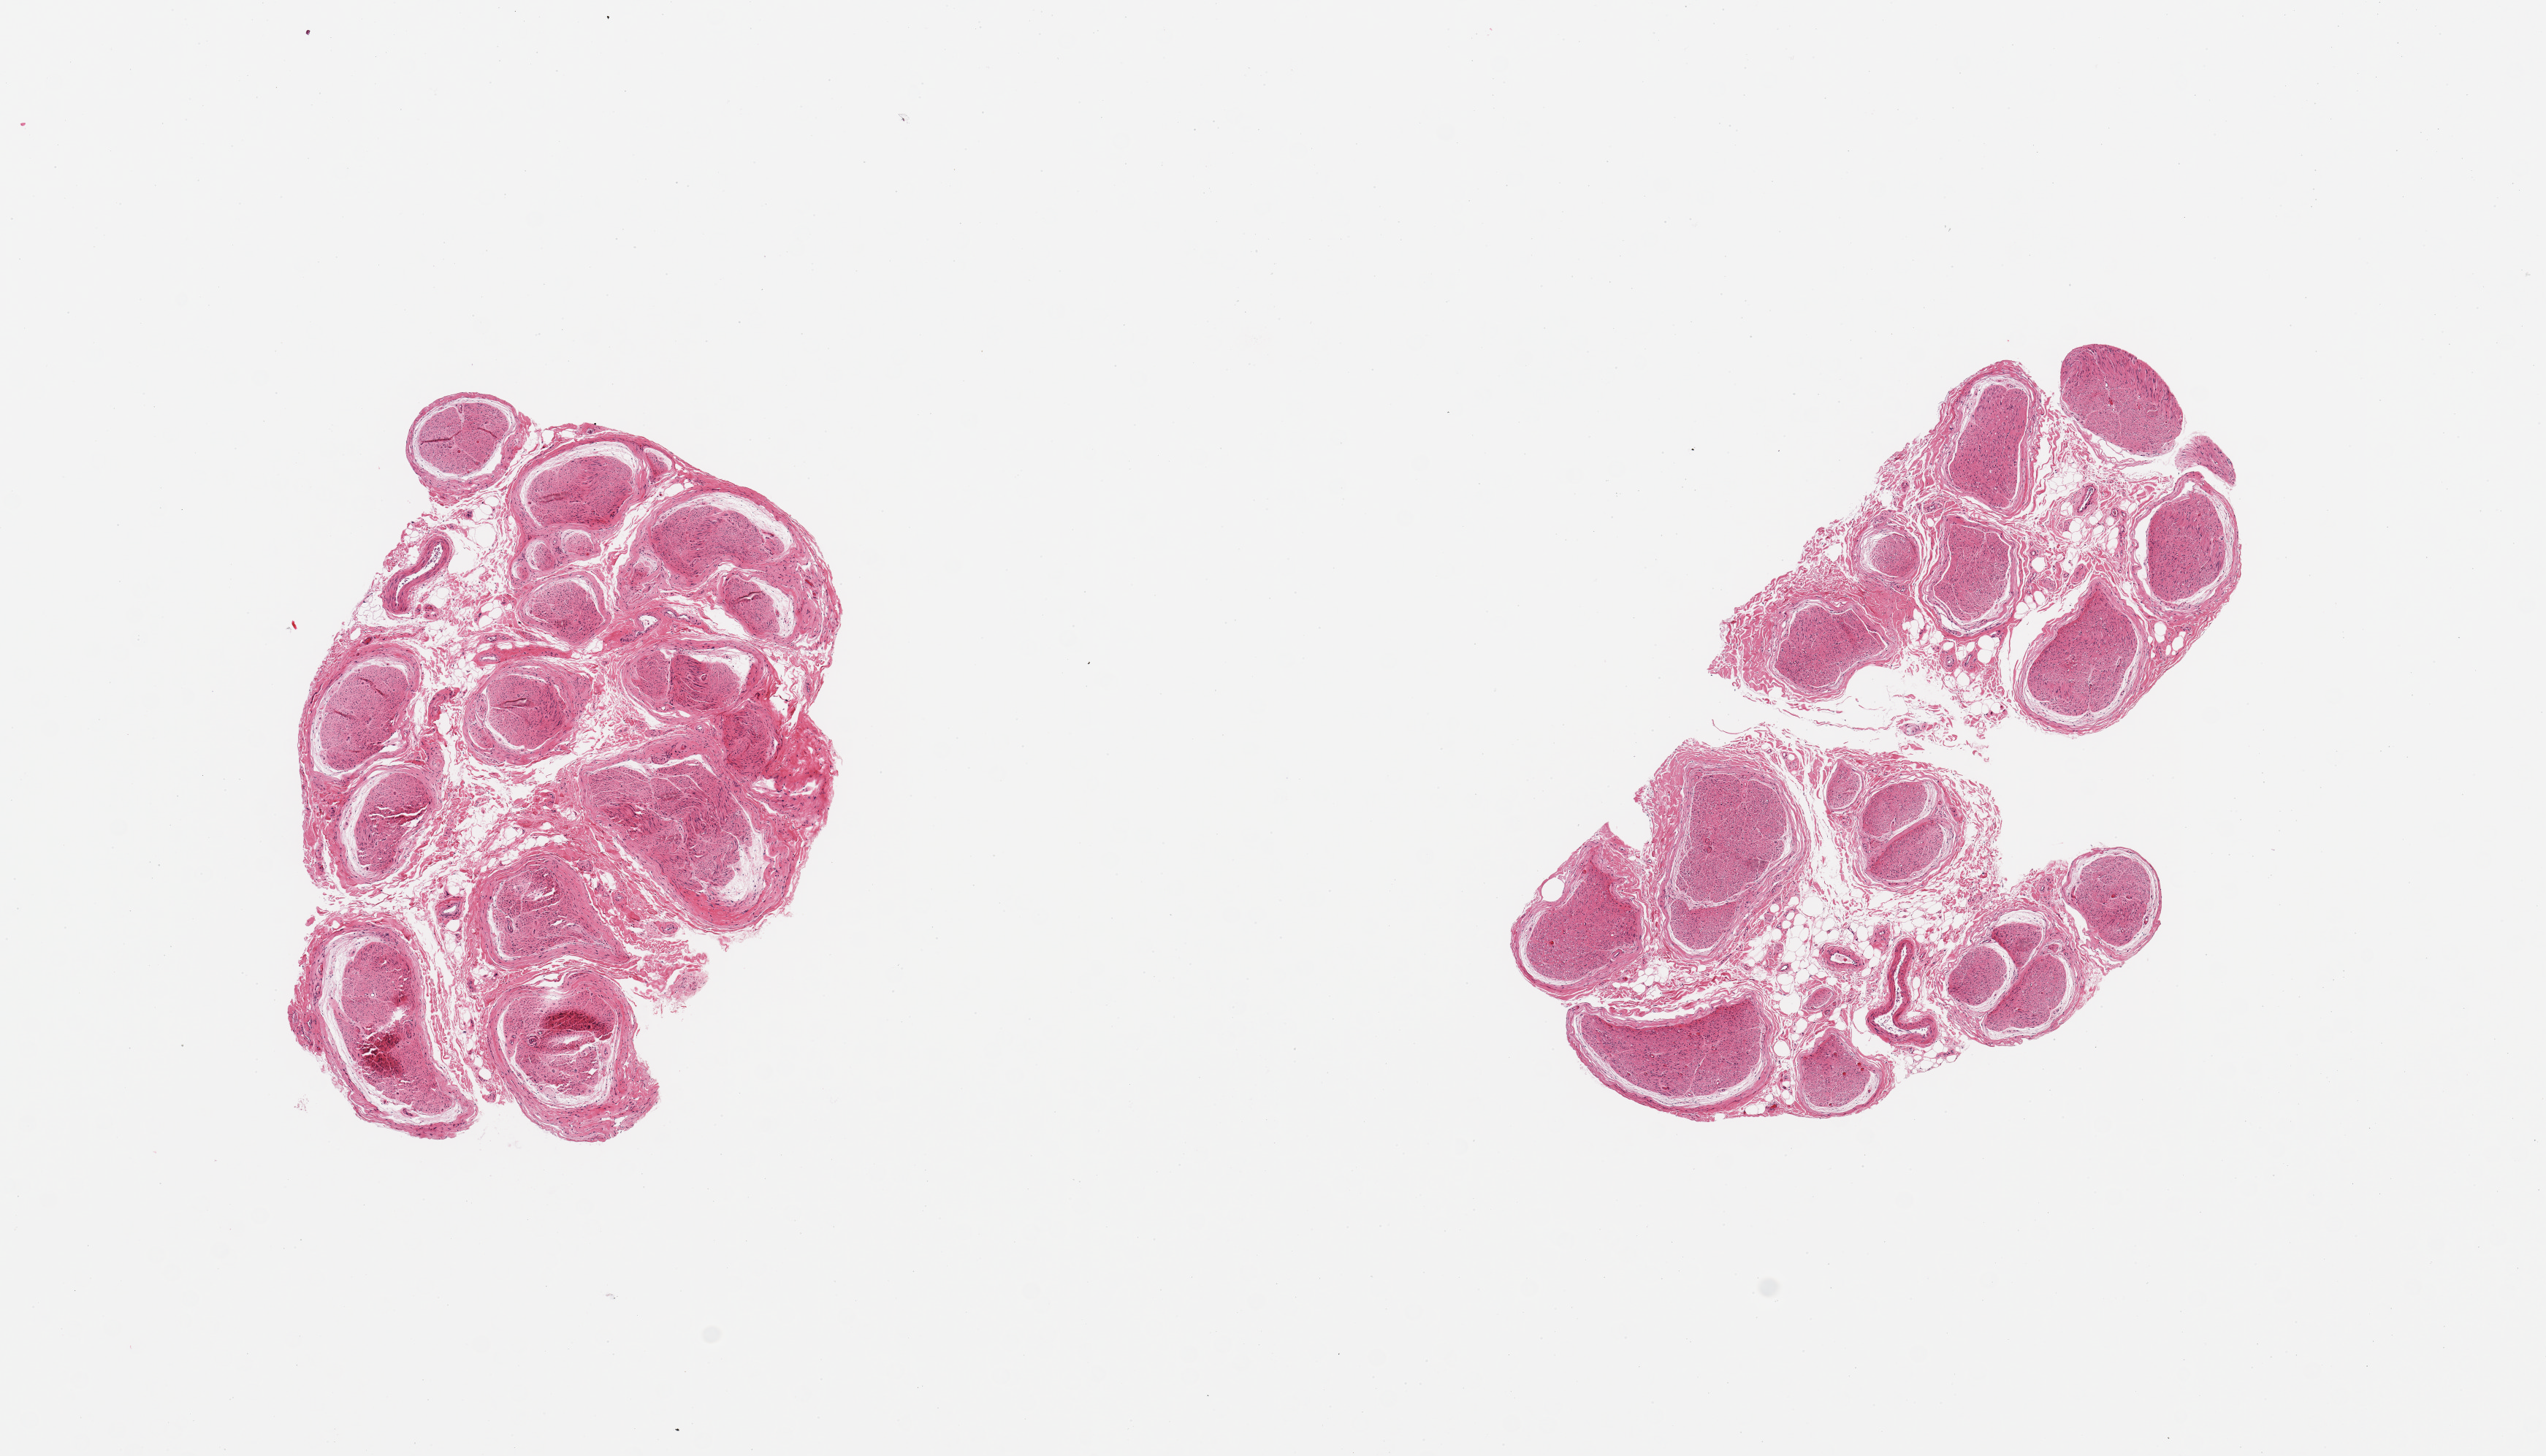
Hematoxylin and eosin (H&E) whole-slide image, a low-resolution overview of the entire scanned area, about 13.8 x 7.9 mm, PAXgene-fixed paraffin-embedded (PFPE) section, section of tibial nerve (target tissue), tissue donor sample.
* reviewer comment on this tissue sample: 2 pieces, no adherent fat